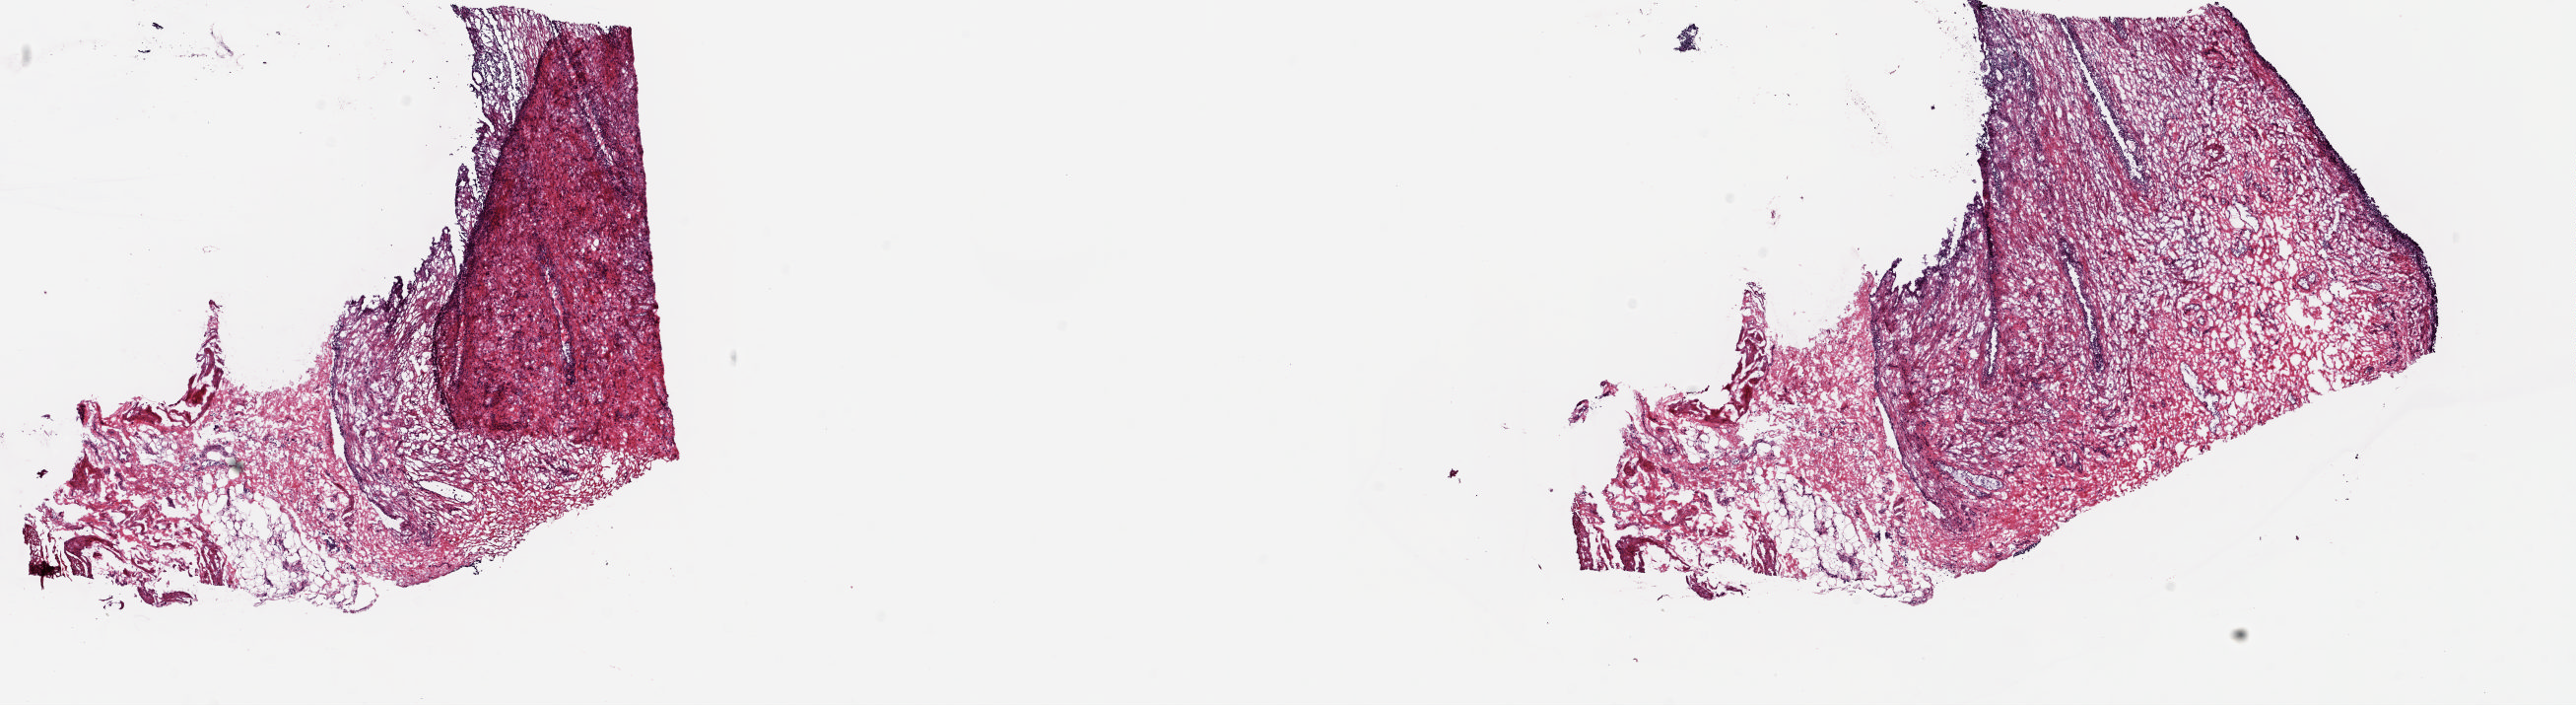
Digitized H&E-stained tissue section (whole slide) — a low-resolution overview of the entire scanned area, about 20.8 x 5.7 mm (from a 20x scan); frozen section; bladder, solid tissue normal (non-tumour tissue) sample. Patient: female, age at initial diagnosis 81 years. Composition of this section per pathologist review: tumour cells 0%, tumour nuclei 0%, normal cells 100%, stromal cells 0%, necrosis 0%. Infiltration values recorded for this section: lymphocyte infiltration 0%, monocyte infiltration 0%, neutrophil infiltration 0%.
This section: solid tissue normal sample (biorepository sample class). Patient diagnosis: Transitional cell carcinoma (trigone of bladder).